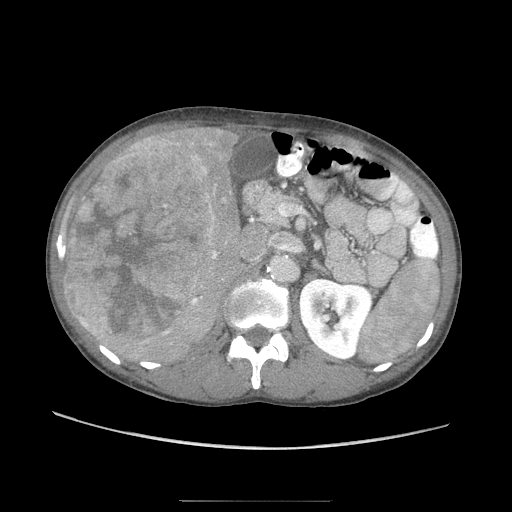
Contrast-enhanced abdominal CT (liver protocol), one axial slice. Position 40 of 103 along the scan axis. Reconstruction kernel STANDARD. Soft-tissue window (W 400 / L 40 HU). 512 × 512 image matrix, field of view 380 × 380 mm. Case-level facts recorded for this patient, not image findings: diagnosis: hepatocellular carcinoma (patient treated with transarterial chemoembolisation; whether this scan precedes or follows treatment is not stated here); TNM stage (as recorded): Stage-IIIA; Child-Pugh class: A; tumour differentiation: moderately differentiated; tumour nodularity: multinodular.
Structures marked on this image (semi-automatic segmentation, software-assisted and operator-edited):
- liver parenchyma outside the tumour (the mass and vessels are separate outlines, so this box may not span the whole liver): bounding box (x1, y1, x2, y2) in pixels: (64, 124, 243, 363)
- mass: (64, 134, 220, 346)
- liver vessels: (82, 143, 212, 326)